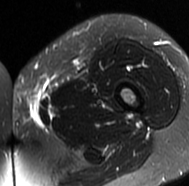
MRI of an extremity soft-tissue mass, one axial slice; slice 20 of 77 in the series (ordered by position); T2-weighted fat-saturated; MR volume resampled by the dataset authors to the PET/CT grid (not the native acquisition matrix); 189 × 186 image matrix, field of view 185 × 182 mm. Female patient. Case-level facts recorded for this patient, not image findings: histological type: leiomyosarcoma; grade: high; site of the primary tumour: groin.
Structures marked on this image (expert contour drawn on MRI and transferred to this co-registered scan by the dataset authors):
- gross tumour volume including surrounding oedema: box from (x=12, y=81) to (x=57, y=126) px